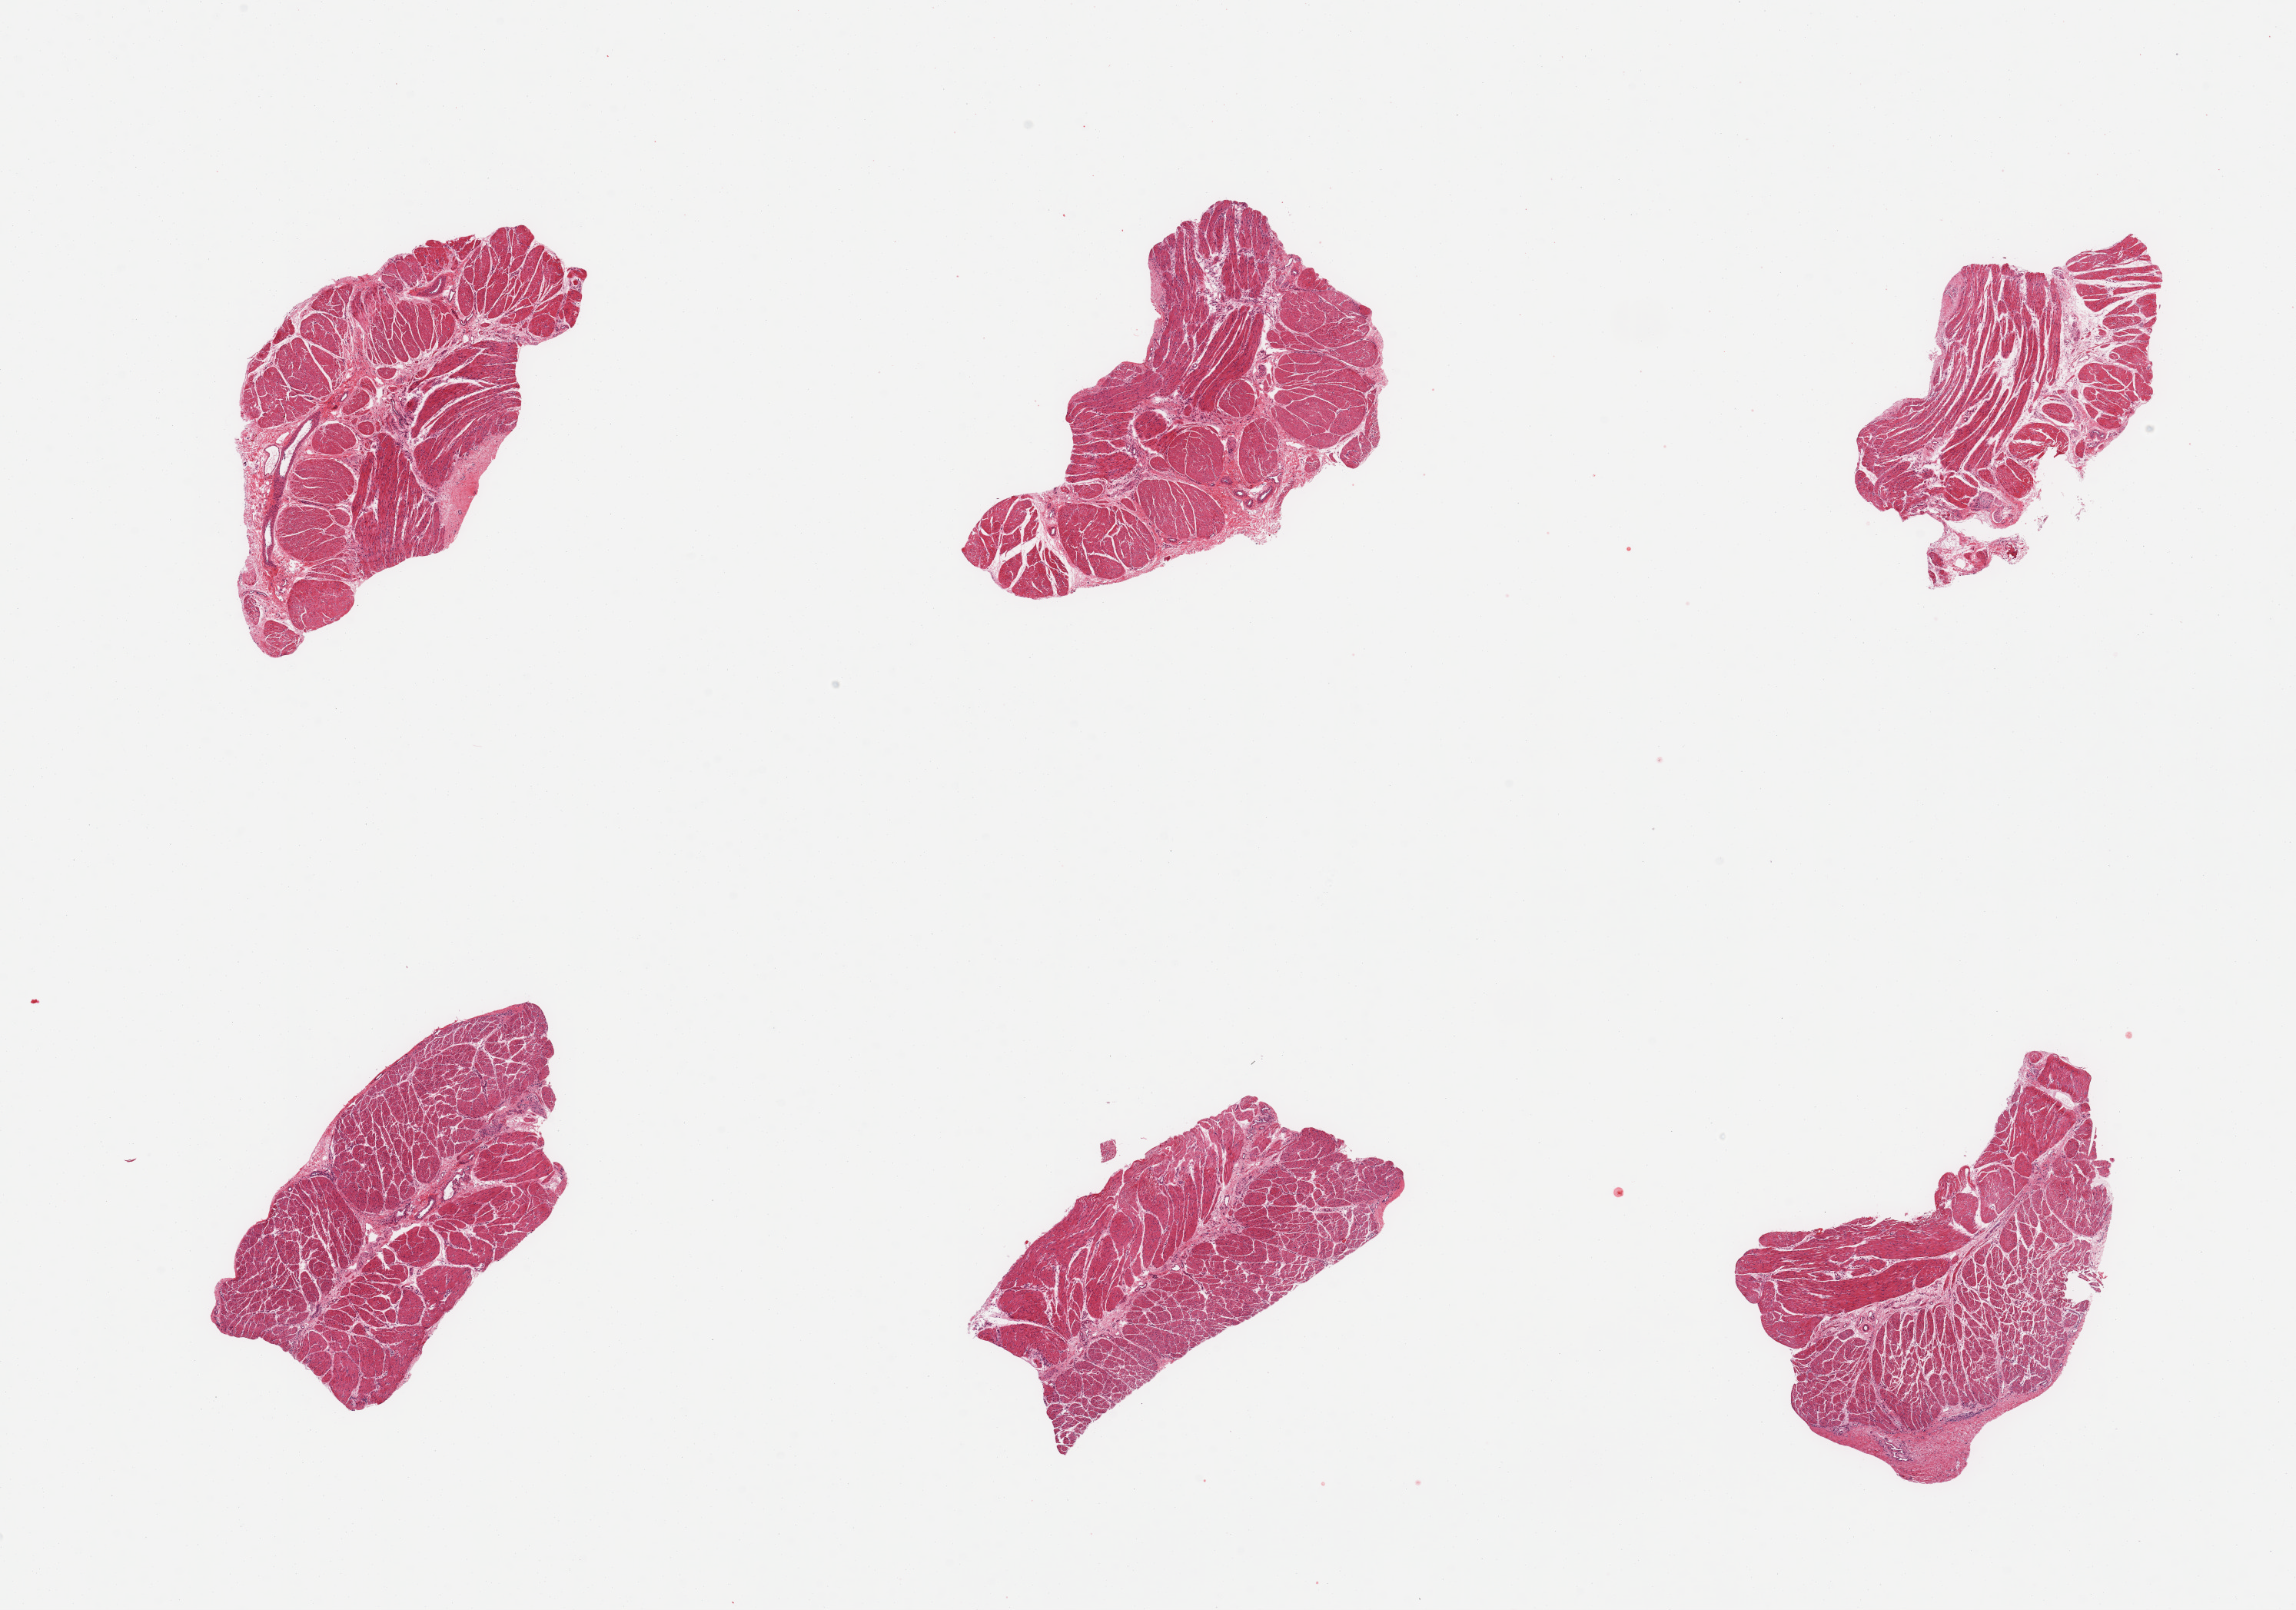
Hematoxylin and eosin (H&E) whole-slide image, a low-resolution overview of the entire scanned area, about 23.6 x 16.6 mm, PAXgene-fixed, paraffin-embedded tissue, section of gastroesophageal junction (target tissue), tissue donor sample. Donor: male.
Pathologist's review note for this sample: 6 pieces, confirmed target muscularis.